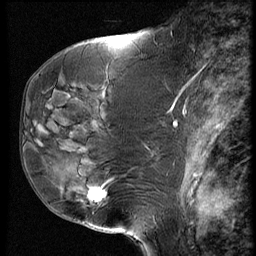
Breast MRI (dynamic contrast-enhanced), one sagittal slice; slice 28 of 60 in the series (ordered by position); dynamic contrast-enhanced series, image 2 of 4 at this slice position (ordered by acquisition); 1.5 T; TE 4.2 ms, TR 9 ms; 256 × 256 image matrix, field of view 180 × 180 mm. Patient: female, 50 years. Case-level facts recorded for this patient, not image findings: setting: breast cancer imaged before/during neoadjuvant chemotherapy; receptor status: HR-positive, HER2-negative.
Outlined on this slice (semi-automatic segmentation, software-assisted and operator-edited):
- analysis volume of interest (the breast-tissue region the enhancement analysis was run in; not a lesion): bounding box <48,109,135,230> (left, top, right, bottom; pixels)
- tumour enhancement mask (voxels above the 140 % enhancement threshold inside the analysis volume of interest): <87,189,106,202>